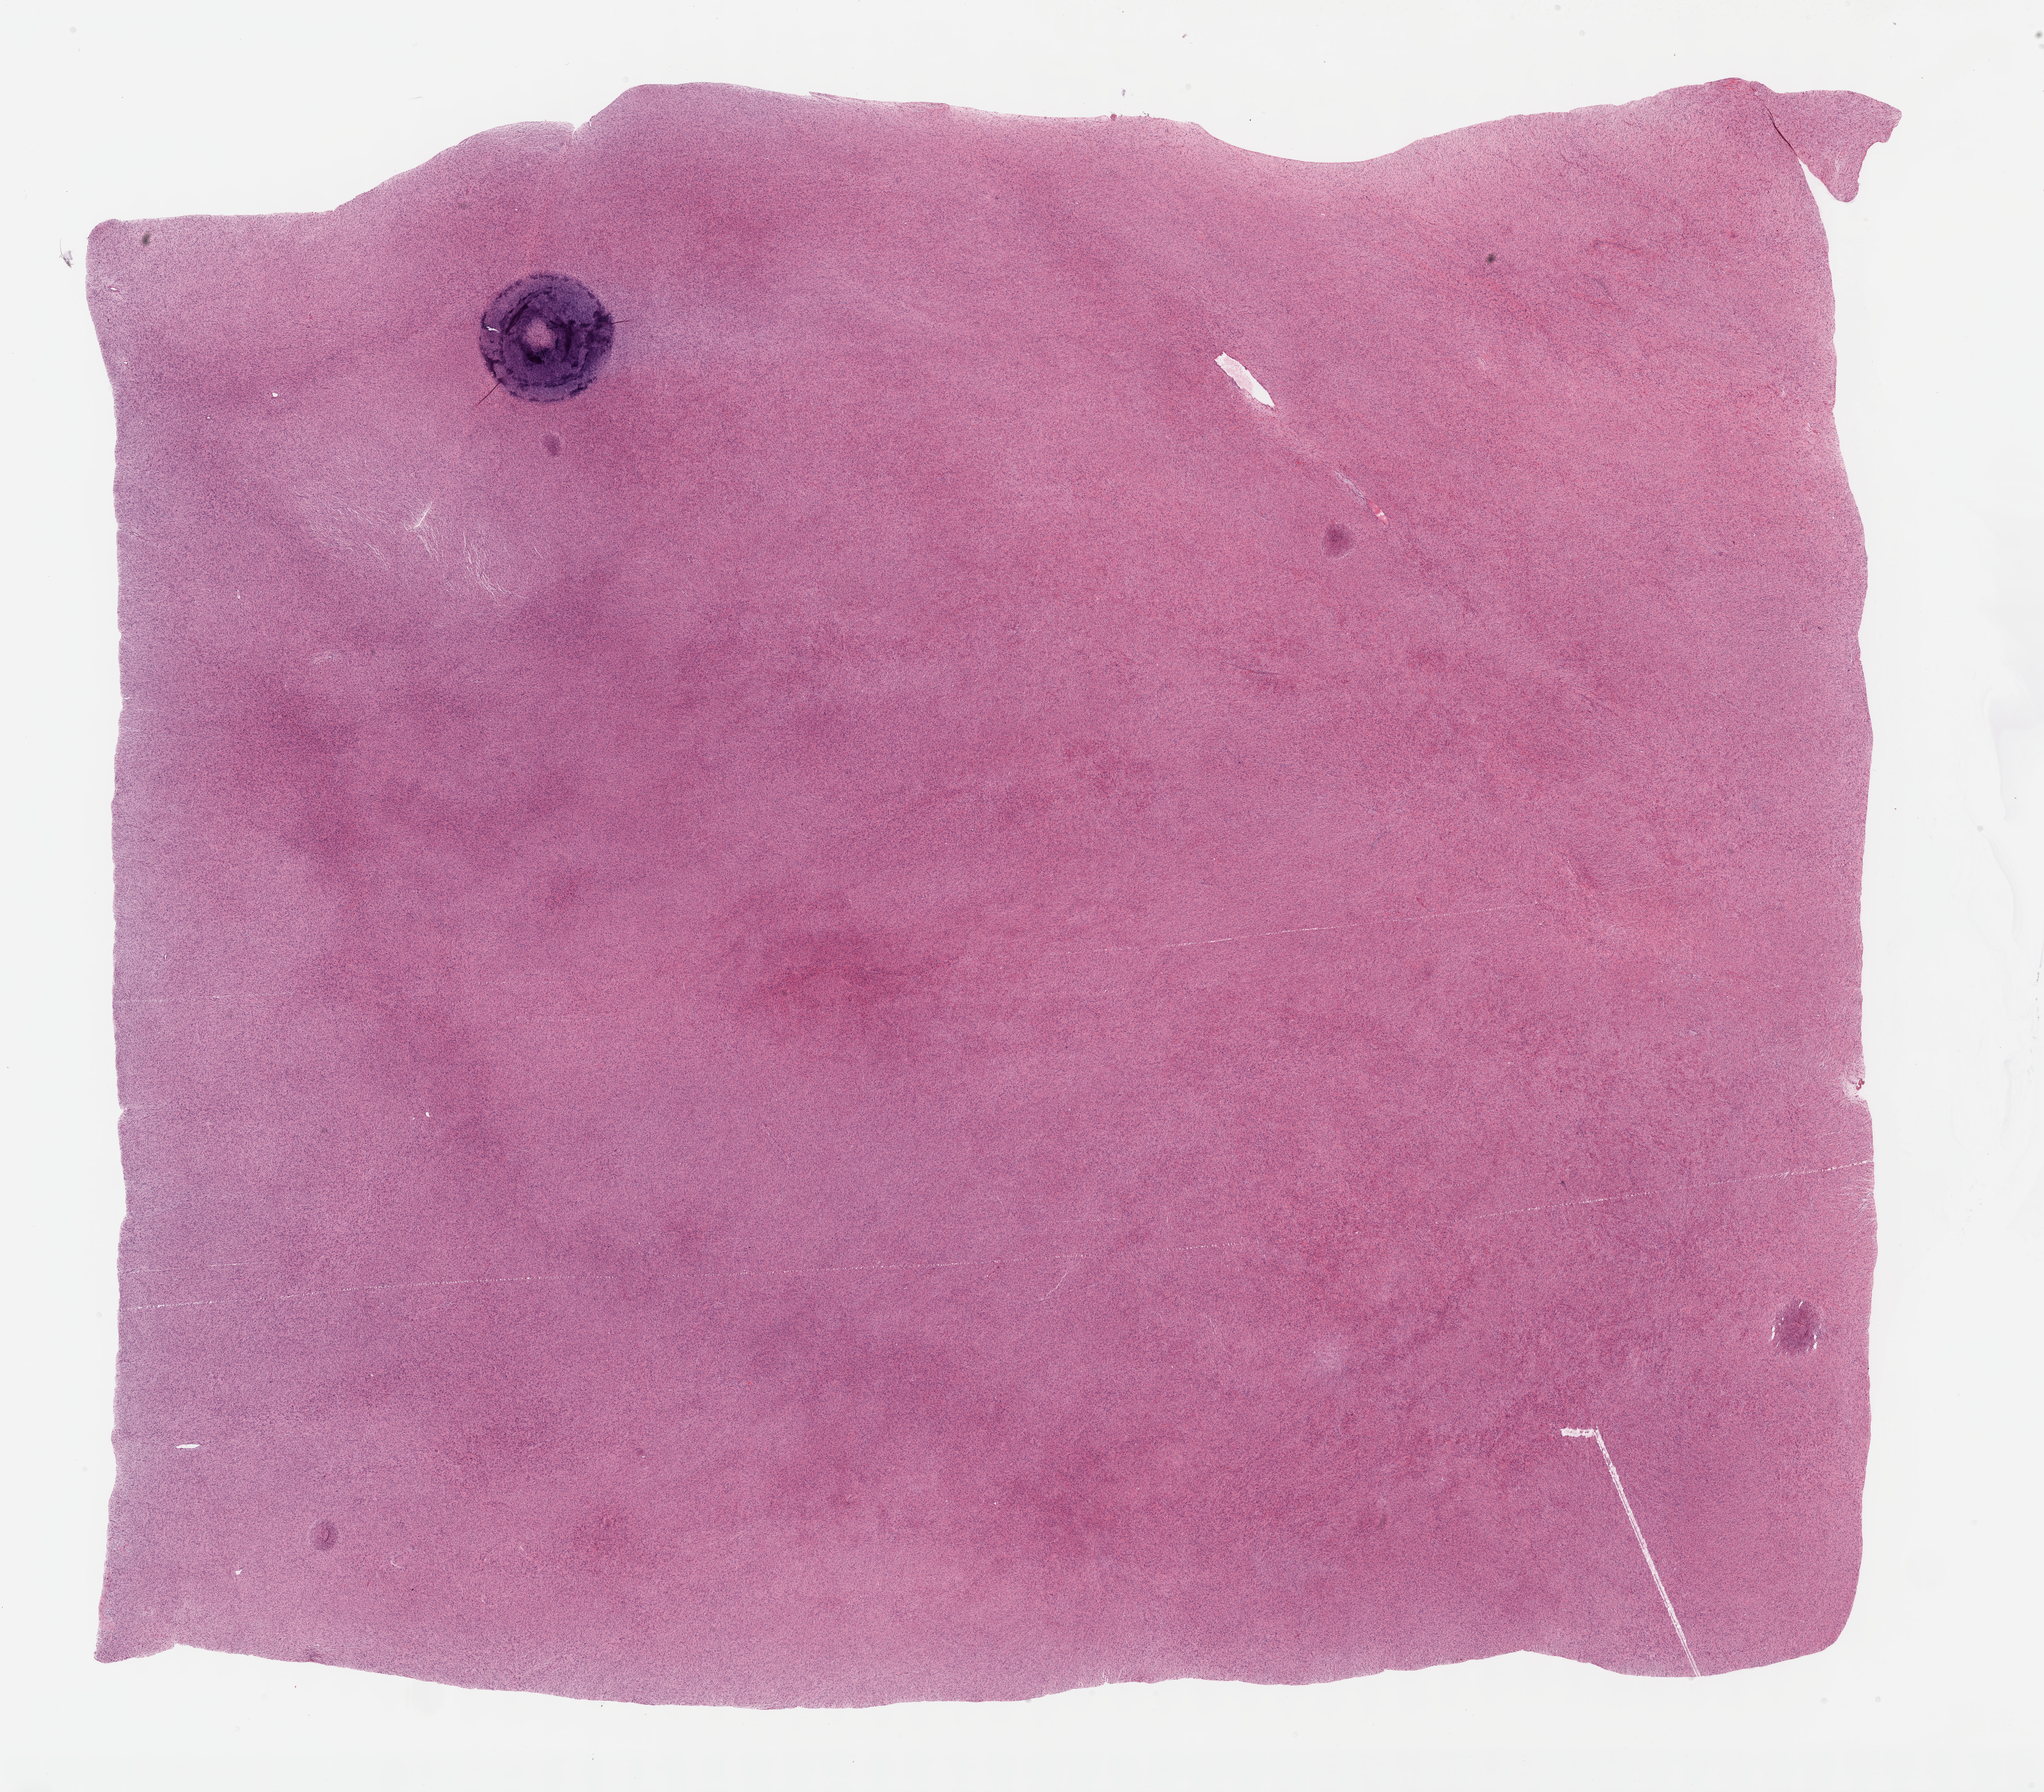
Hematoxylin and eosin (H&E) stained whole-slide image, whole scanned area (about 25.2 x 22.1 mm, from a 40x scan) shown as a low-resolution overview; formalin-fixed paraffin-embedded (FFPE) diagnostic section; primary tumour sample from the retroperitoneum and peritoneum. Patient: male, age at initial diagnosis 58 years.
- histologic diagnosis: Dedifferentiated liposarcoma